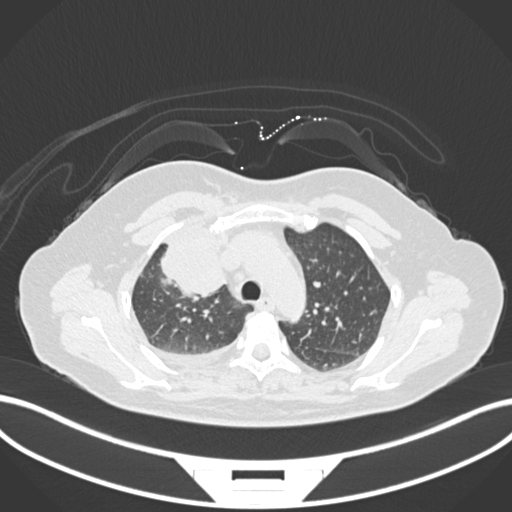
Chest CT, one axial slice. Slice 119 of 172 in the series (ordered by position). Lung window (W 1500 / L -600 HU). 512 × 512 image matrix, field of view 400 × 400 mm. Female patient, age 52 years. Case-level facts recorded for this patient, not image findings: clinical TNM (as recorded): T3 N1 M1.
Annotated regions visible in this slice (bounding box drawn by a radiologist):
- lung tumour (recorded histology: adenocarcinoma): bounding box <159,226,230,301> (left, top, right, bottom; pixels)